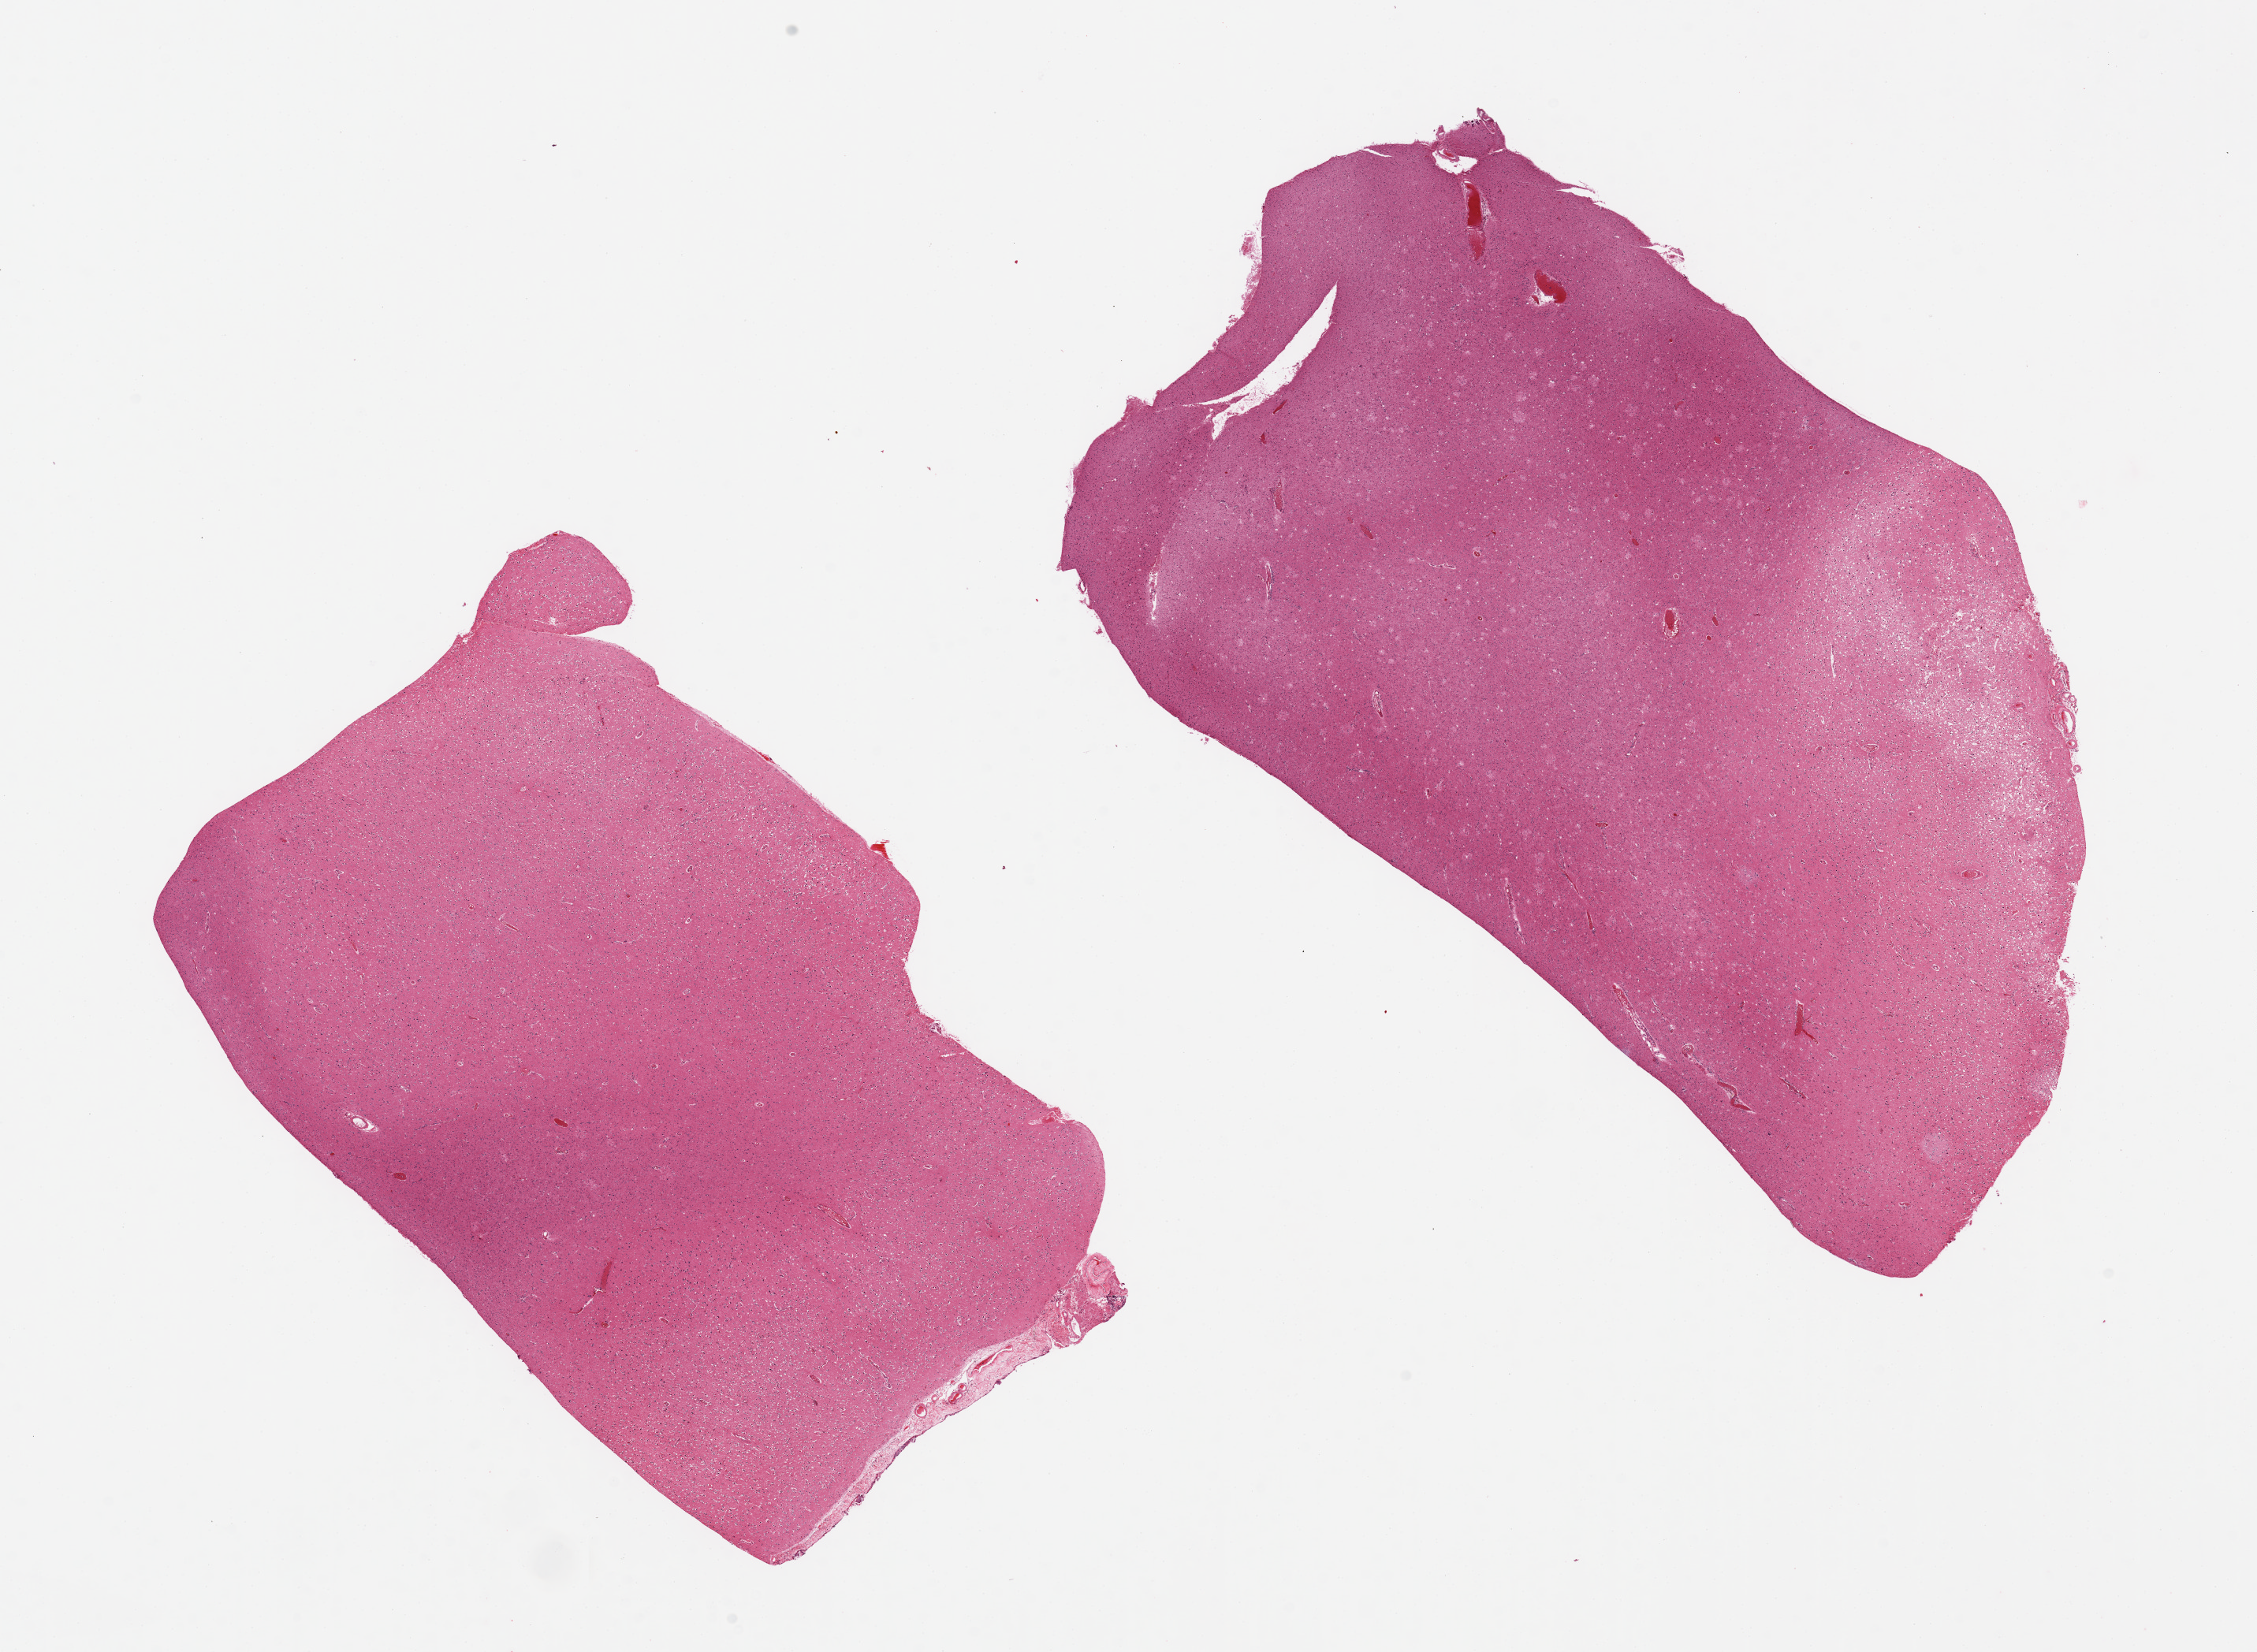
Hematoxylin and eosin (H&E) whole-slide image — whole scanned area (about 22.6 x 16.6 mm) shown as a low-resolution overview, PAXgene-fixed, paraffin-embedded tissue, section of cerebral cortex (target tissue), donor tissue sample.
- pathologist's review note for this sample: 2 pieces, no abnormalities